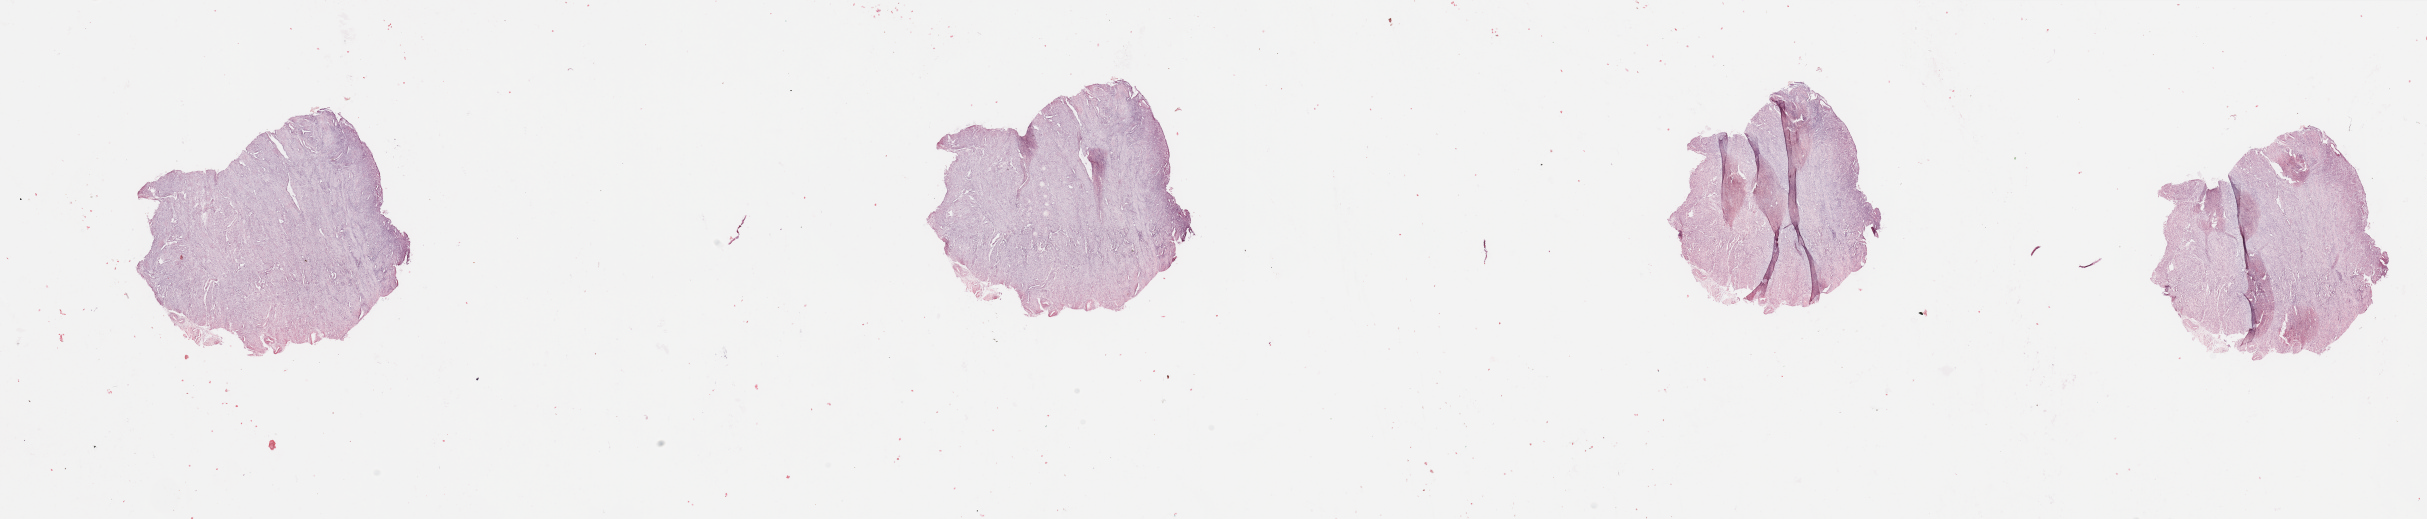
Digitized Hematoxylin and eosin (H&E) stained tissue section (whole slide), a low-resolution overview of the entire scanned area, about 38.4 x 8.2 mm (from a 20x scan); normal (non-tumour) tissue sample, sampled site: uterus. Patient: female, age 60 years.
This section: normal (non-tumour) tissue from the same patient. Patient diagnosis: Endometrioid adenocarcinoma, NOS.